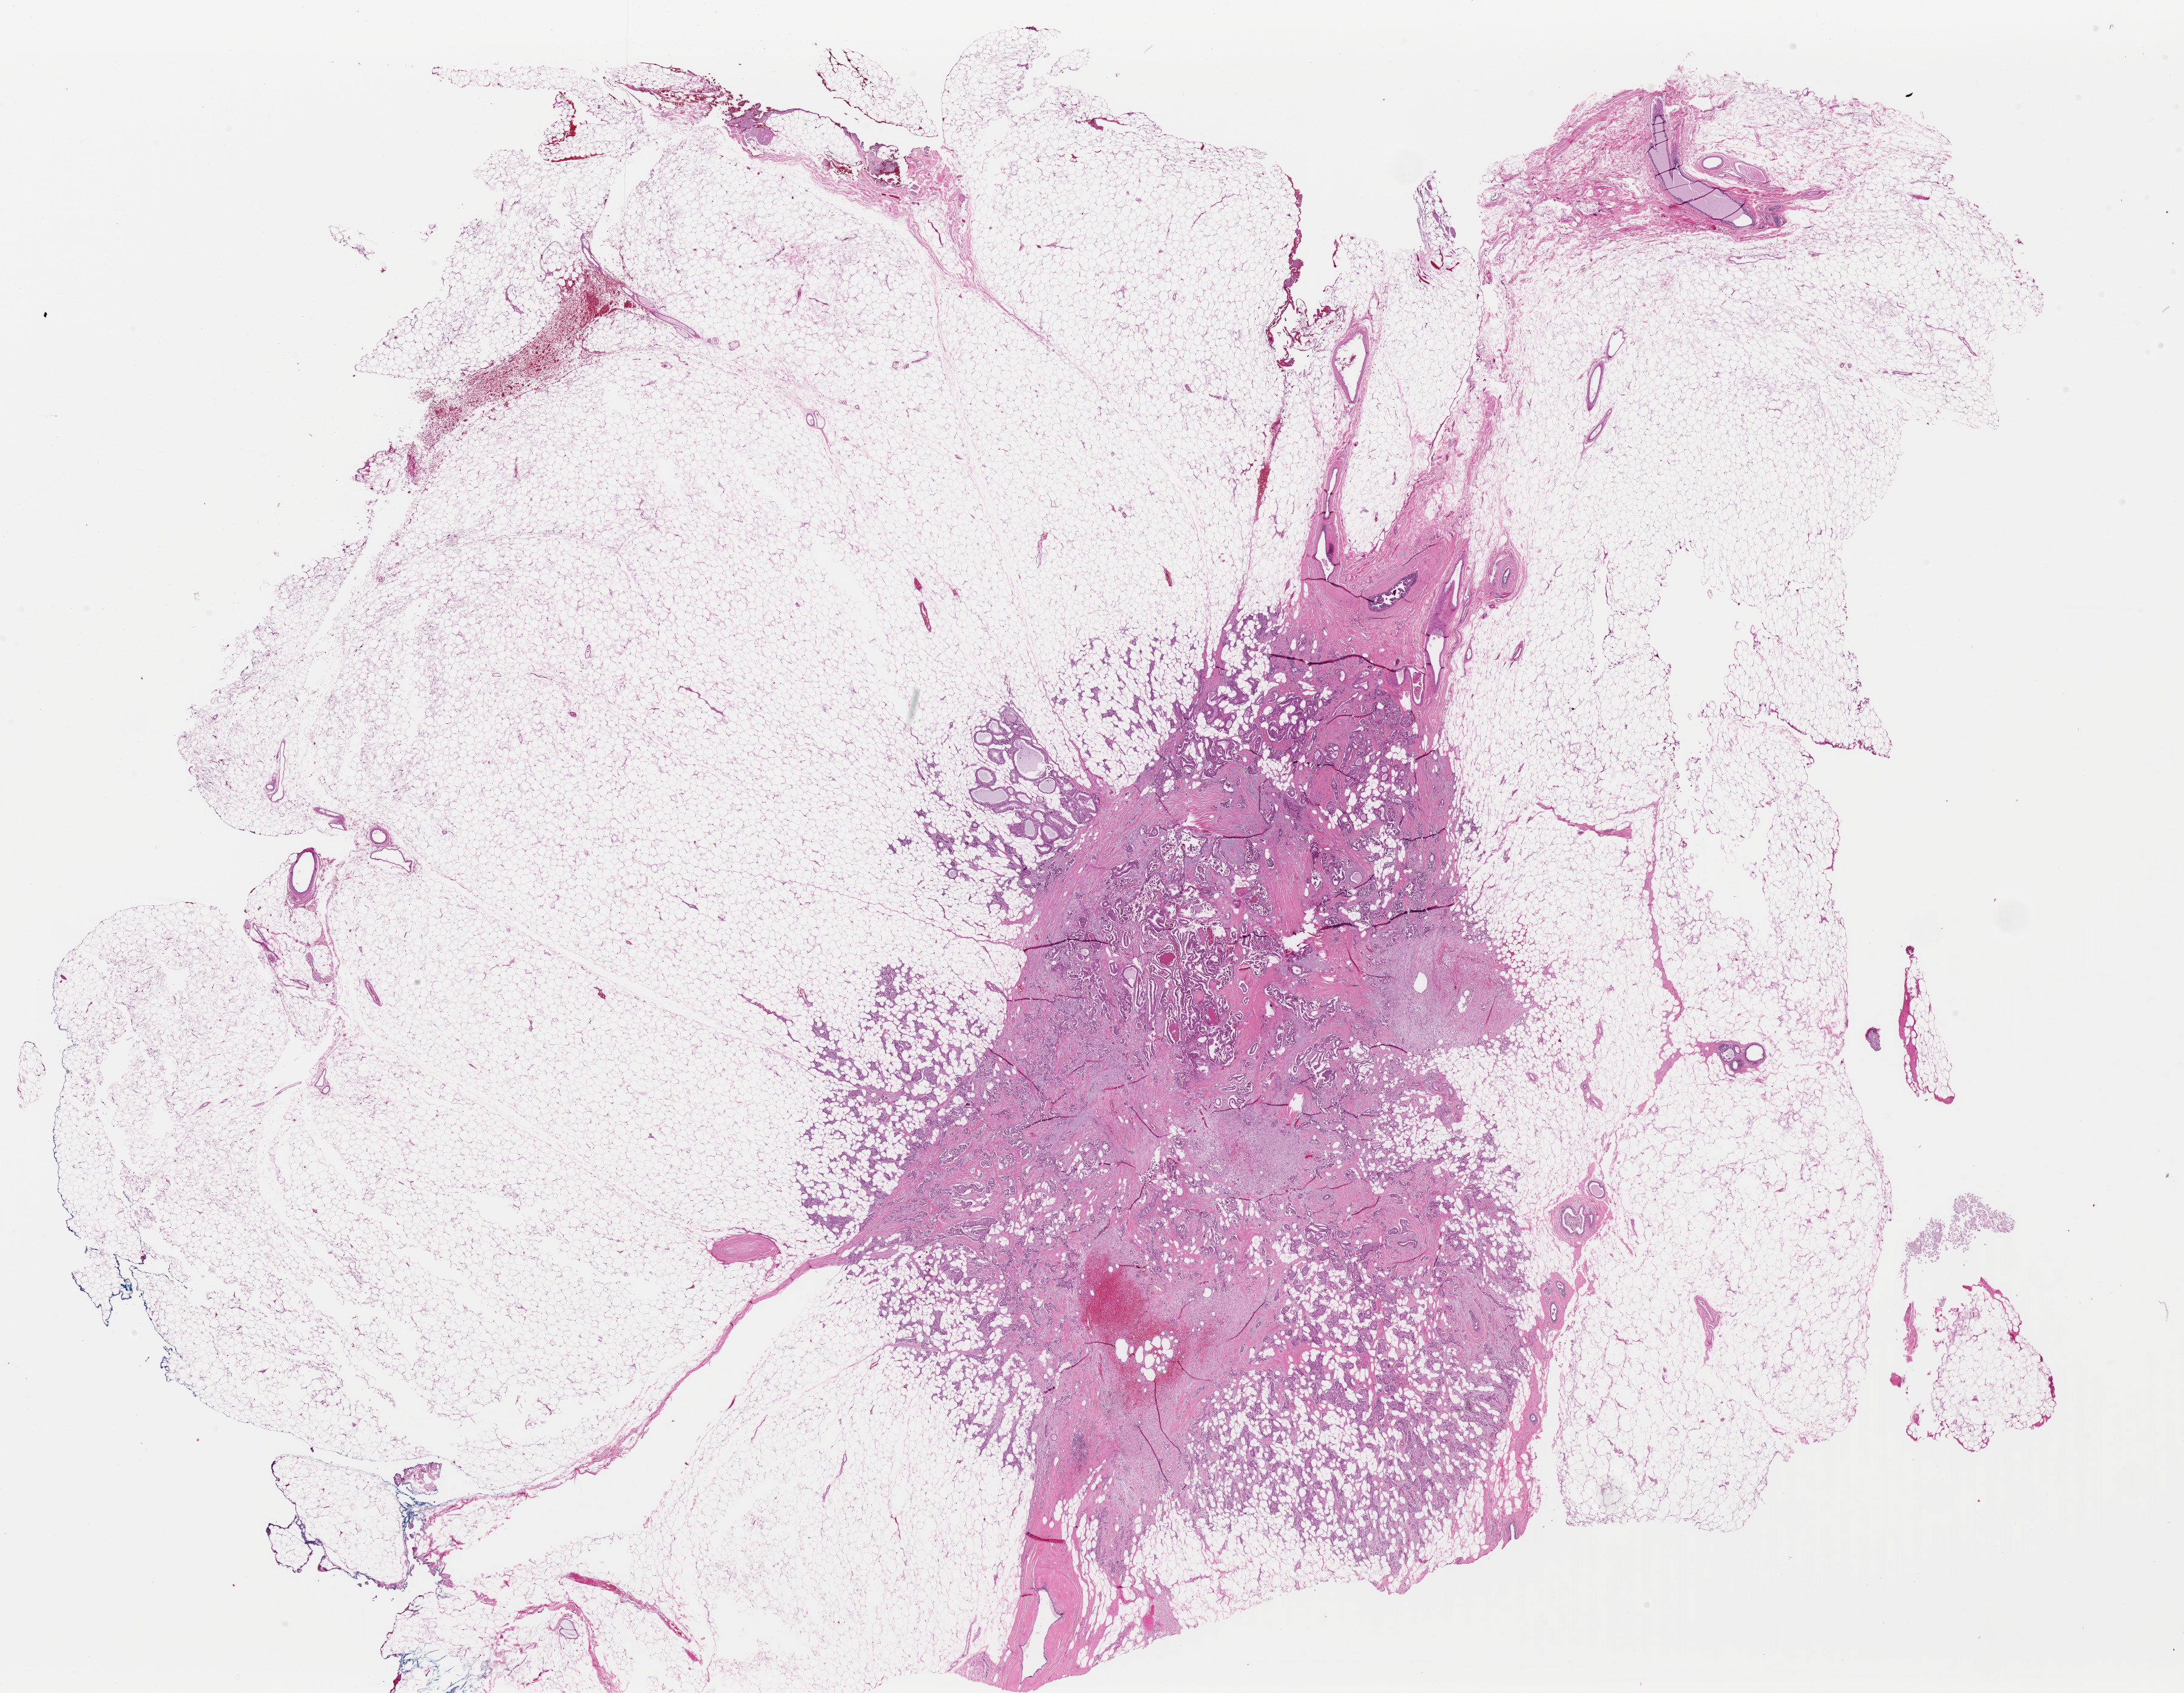
Whole-slide histology image, H&E-stained — a low-resolution overview of the entire scanned area, about 28.4 x 22.0 mm (slide scanned at 40x), formalin-fixed paraffin-embedded (FFPE) diagnostic section, primary tumour sample from the breast. Patient: female, age at initial diagnosis 63 years.
Pathologic diagnosis: Infiltrating duct carcinoma, NOS.